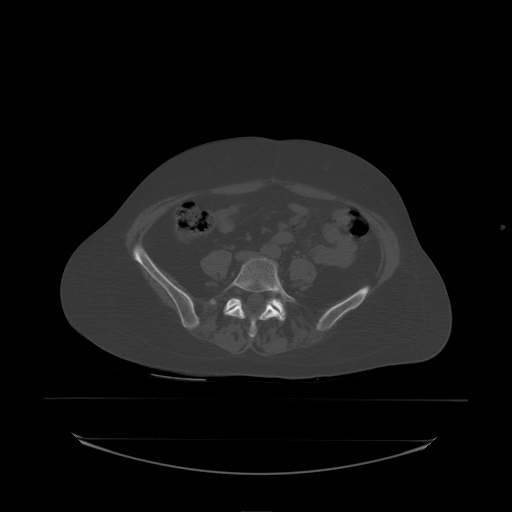
CT including the spine, one axial slice. Slice 38 of 242 in the series (ordered by position). Bone window (W 1800 / L 400 HU). 512 × 512 image matrix, field of view 500 × 500 mm. Female patient, age 53 years. From the clinical record (not read from this slice): primary cancer: lung.
Outlined on this slice (semi-automatic segmentation, software-assisted and operator-edited):
- L5 vertebra: bounding box <224,258,296,338> (left, top, right, bottom; pixels)